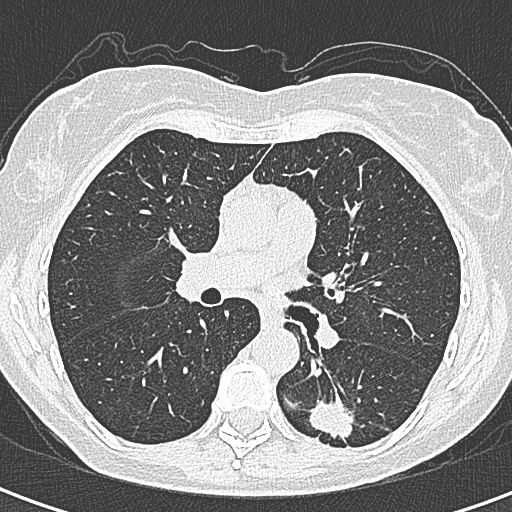
Low-dose screening chest CT, axial slice, baseline annual screen, lung window (W 1500 / L -600 HU), 1 mm slice thickness, slice 135 of 328 in the series, 512 × 512 image matrix. Female, age 58 years at enrolment.
Expert reader's lesion annotation, bounding box <297,387,366,456> (left, top, right, bottom; pixels). The screening reader recorded 2 non-calcified nodules or masses ≥4 mm on this exam; which of them this box marks is not recorded. Participant outcome: lung cancer diagnosed 22 days after this screen — adenocarcinoma, NOS, left lower lobe, moderately differentiated (G2), stage IA (AJCC 6th edition), 25 mm at pathology.